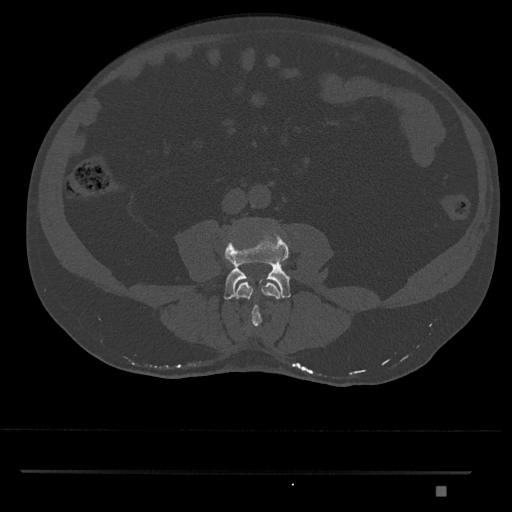
CT including the spine, one axial slice. Position 642 of 1134 along the scan axis. Reconstruction kernel Br40s/3. 120 kVp. Bone window (W 1800 / L 400 HU). 0.5 mm slice thickness. 512 × 512 image matrix, field of view 429 × 429 mm. Male patient, age 65 years. From the clinical record (not read from this slice): primary cancer: prostate.
Structures marked on this image (semi-automatically segmented with operator editing):
- L3 vertebra: bounding box [x1, y1, x2, y2] px = [236, 282, 280, 327]
- L4 vertebra: [224, 227, 291, 300]